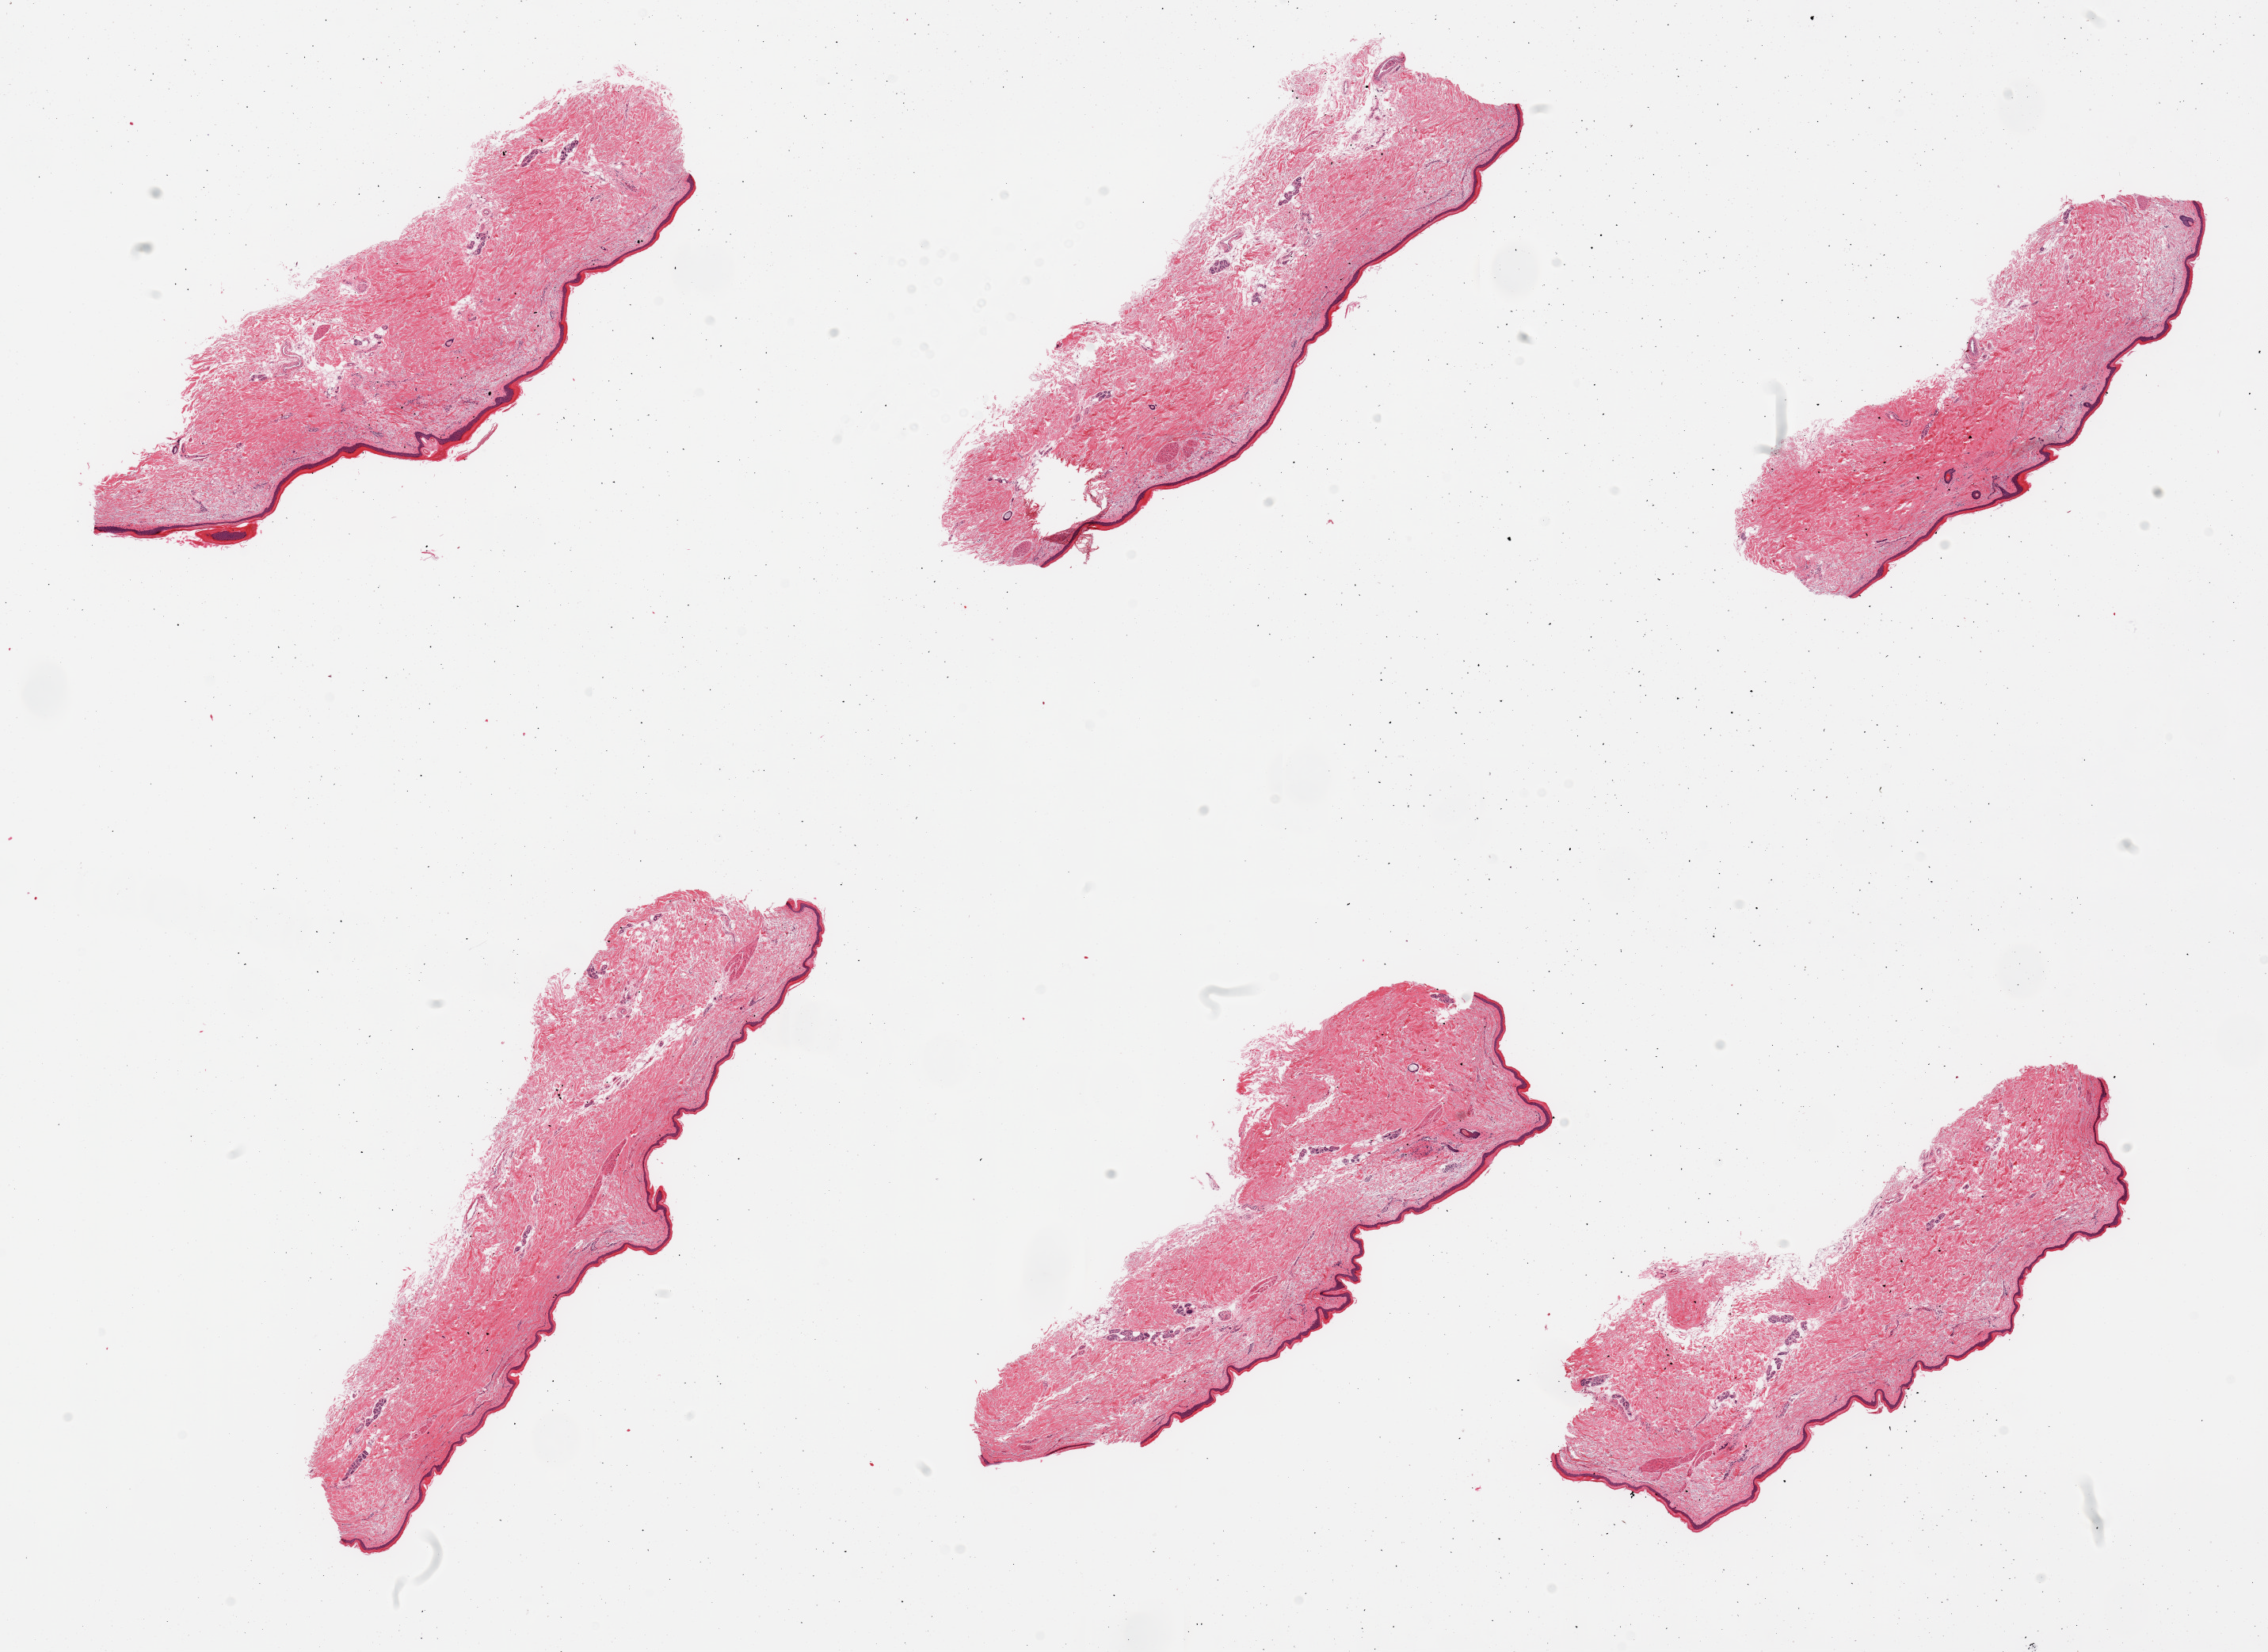
Whole-slide image, H&E stain, brightfield — shown as a low-resolution overview of the whole scanned area (about 22.6 x 16.5 mm), PAXgene-fixed, paraffin-embedded tissue, section of skin of lower leg (target tissue), tissue donor sample. Donor: female.
* reviewer comment on this tissue sample: pieces; 5% dermal fat; well trimmed